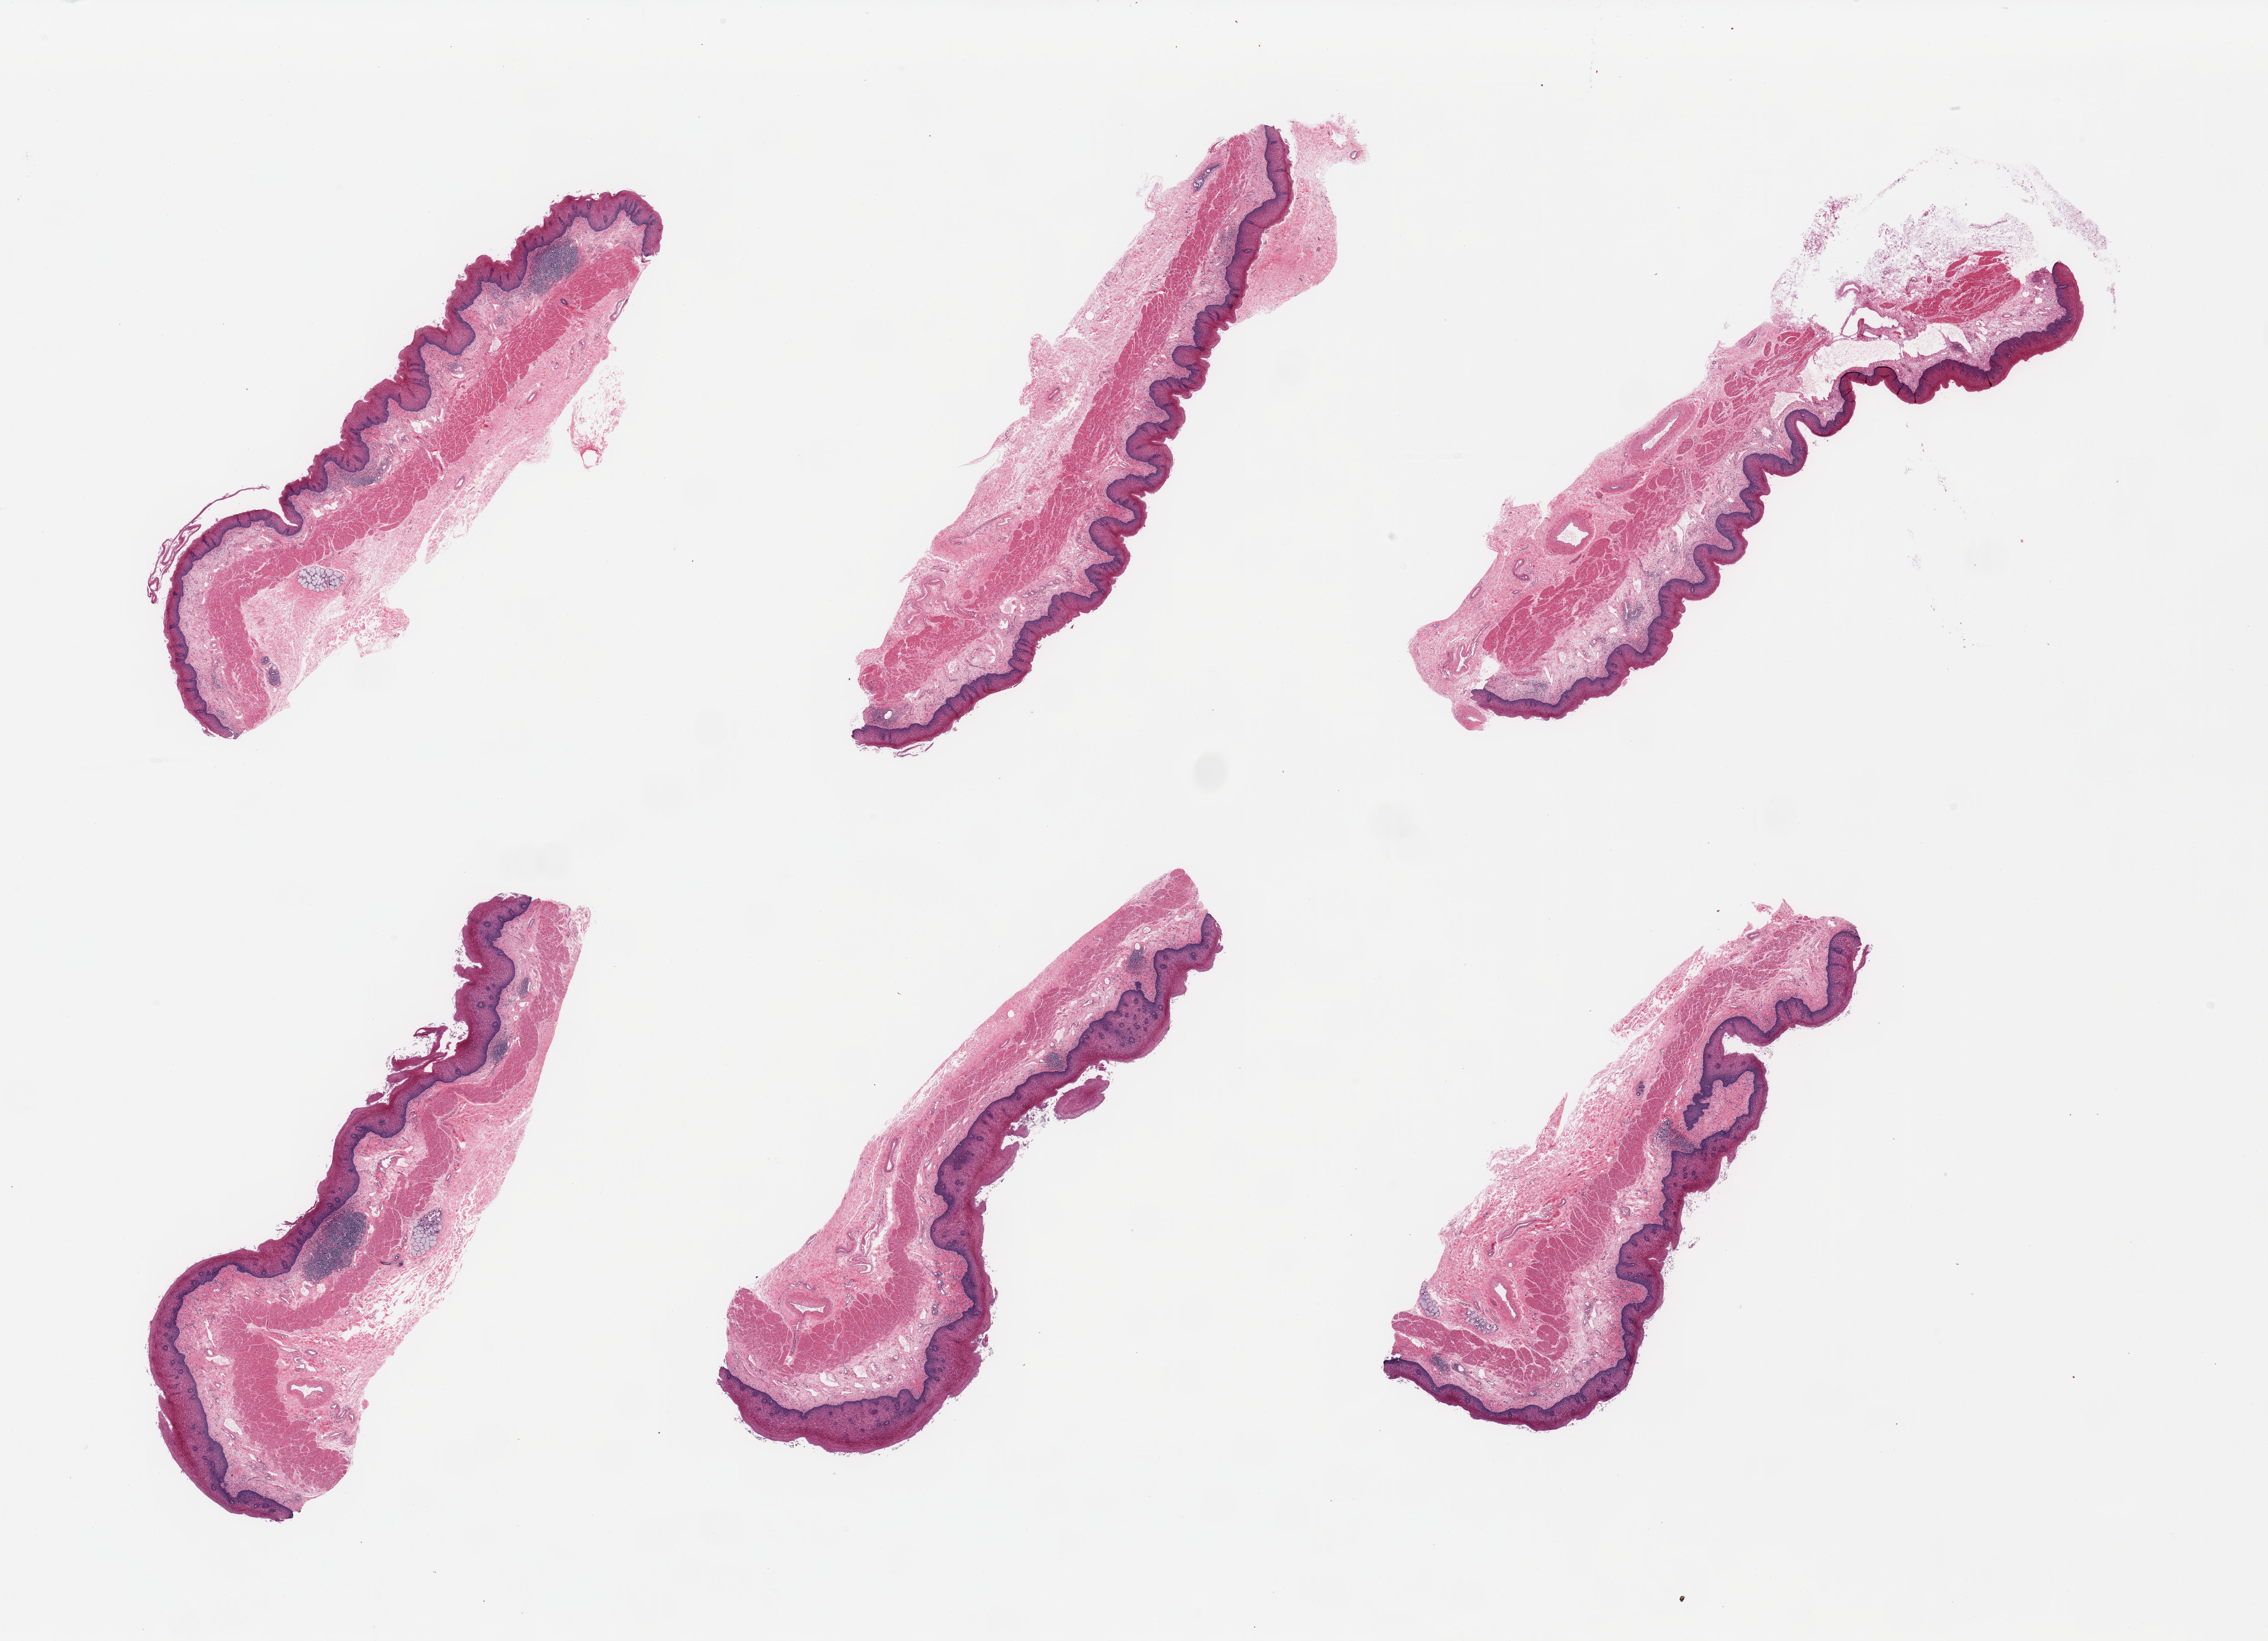
H&E whole-slide image, brightfield, low-resolution overview of the scanned area, about 30.5 x 22.1 mm (from a 20x scan); PAXgene-fixed paraffin-embedded (PFPE) section; section of esophageal mucous membrane (target tissue); tissue donor sample. Donor sex: male.
Reviewer comment on this tissue sample: 6 pieces; includes few lymphoid aggregates and clusters of submucosal glands.